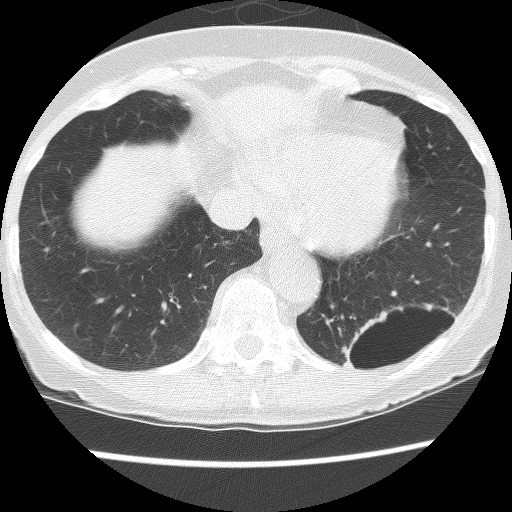
Axial slice from a low-dose chest CT screening exam, third screening round (two years after baseline), lung window (W 1500 / L -600 HU), 2.5 mm slice thickness, 512 × 512 image matrix, field of view 290 × 290 mm. Female participant, aged 61 years at enrolment.
Expert-annotated lung lesion, bounding box [x1, y1, x2, y2] px = [334, 293, 443, 386]. The screening reader recorded 2 non-calcified nodules or masses ≥4 mm on this exam; which of them this box marks is not recorded. Official screen result: positive, no significant change: stable abnormalities potentially related to lung cancer, unchanged since the prior screening exam. Lung cancer was diagnosed 166 days after this screen: non-small cell carcinoma, left lower lobe, poorly differentiated (G3), stage IB (AJCC 6th edition), 100 mm at pathology.